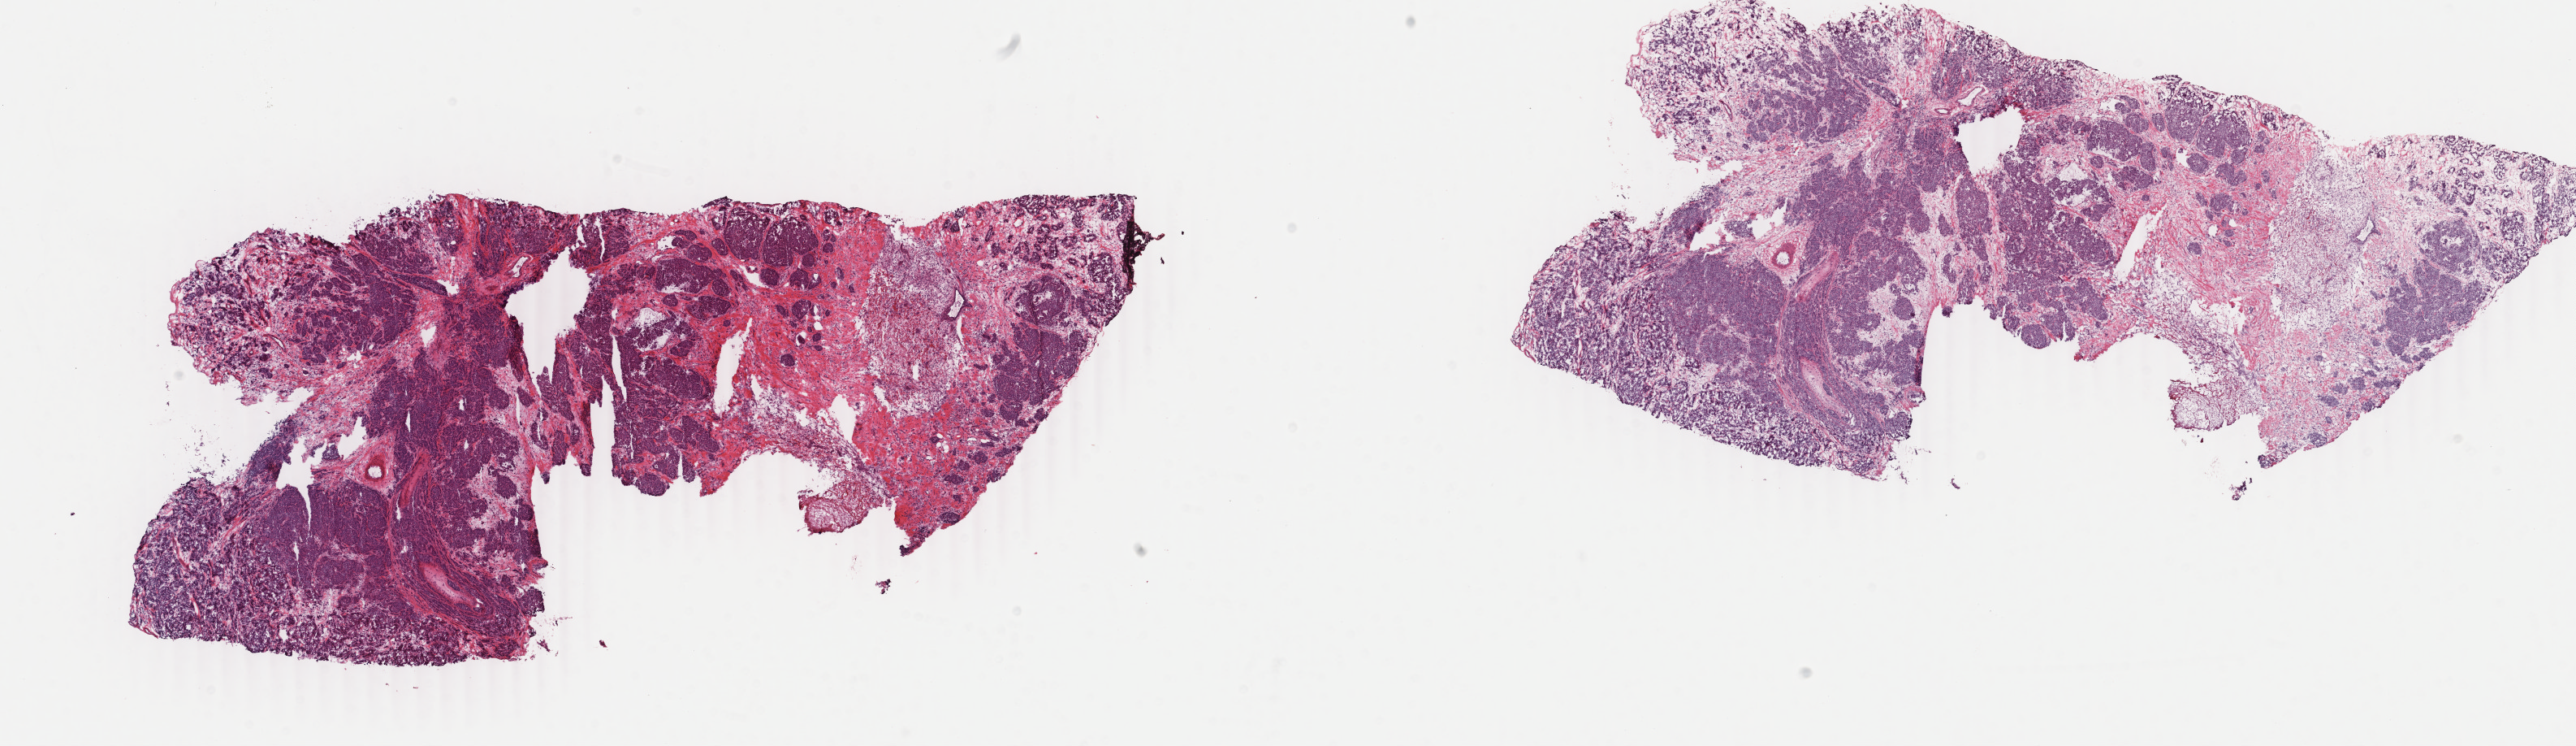
Whole-slide histology image, H&E — shown as a low-resolution overview of the whole scanned area (about 25.2 x 7.3 mm, slide scanned at 40x). Frozen section. Sample: primary tumour, breast. Female patient; age at initial diagnosis 61 years. Pathologist review of this section (percent, as recorded): tumour cells 49%, tumour nuclei 85%, normal cells 2%, stromal cells 48%, necrosis 1%. Infiltration values recorded for this section: lymphocyte infiltration 3%, monocyte infiltration 1%, neutrophil infiltration 0%.
Histologic diagnosis: Infiltrating duct carcinoma, NOS. AJCC pathologic stage: IIIA (6th edition). Lymph nodes positive (case pathology): 4 of 15 examined.